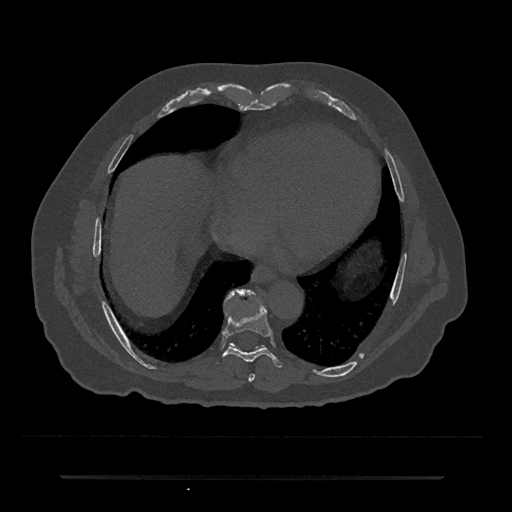
CT including the spine, one axial slice. Position 322 of 797 along the scan axis. Reconstruction kernel Br40s/3. Bone window (W 1800 / L 400 HU). 512 × 512 image matrix. Patient: male, 69 years. From the clinical record (not read from this slice): primary cancer: prostate.
Annotated regions visible in this slice (semi-automatically segmented with operator editing):
- T7 vertebra: box from (x=248, y=374) to (x=255, y=382) px
- T8 vertebra: (x=222, y=303)–(x=283, y=368)
- T9 vertebra: (x=229, y=289)–(x=253, y=300)